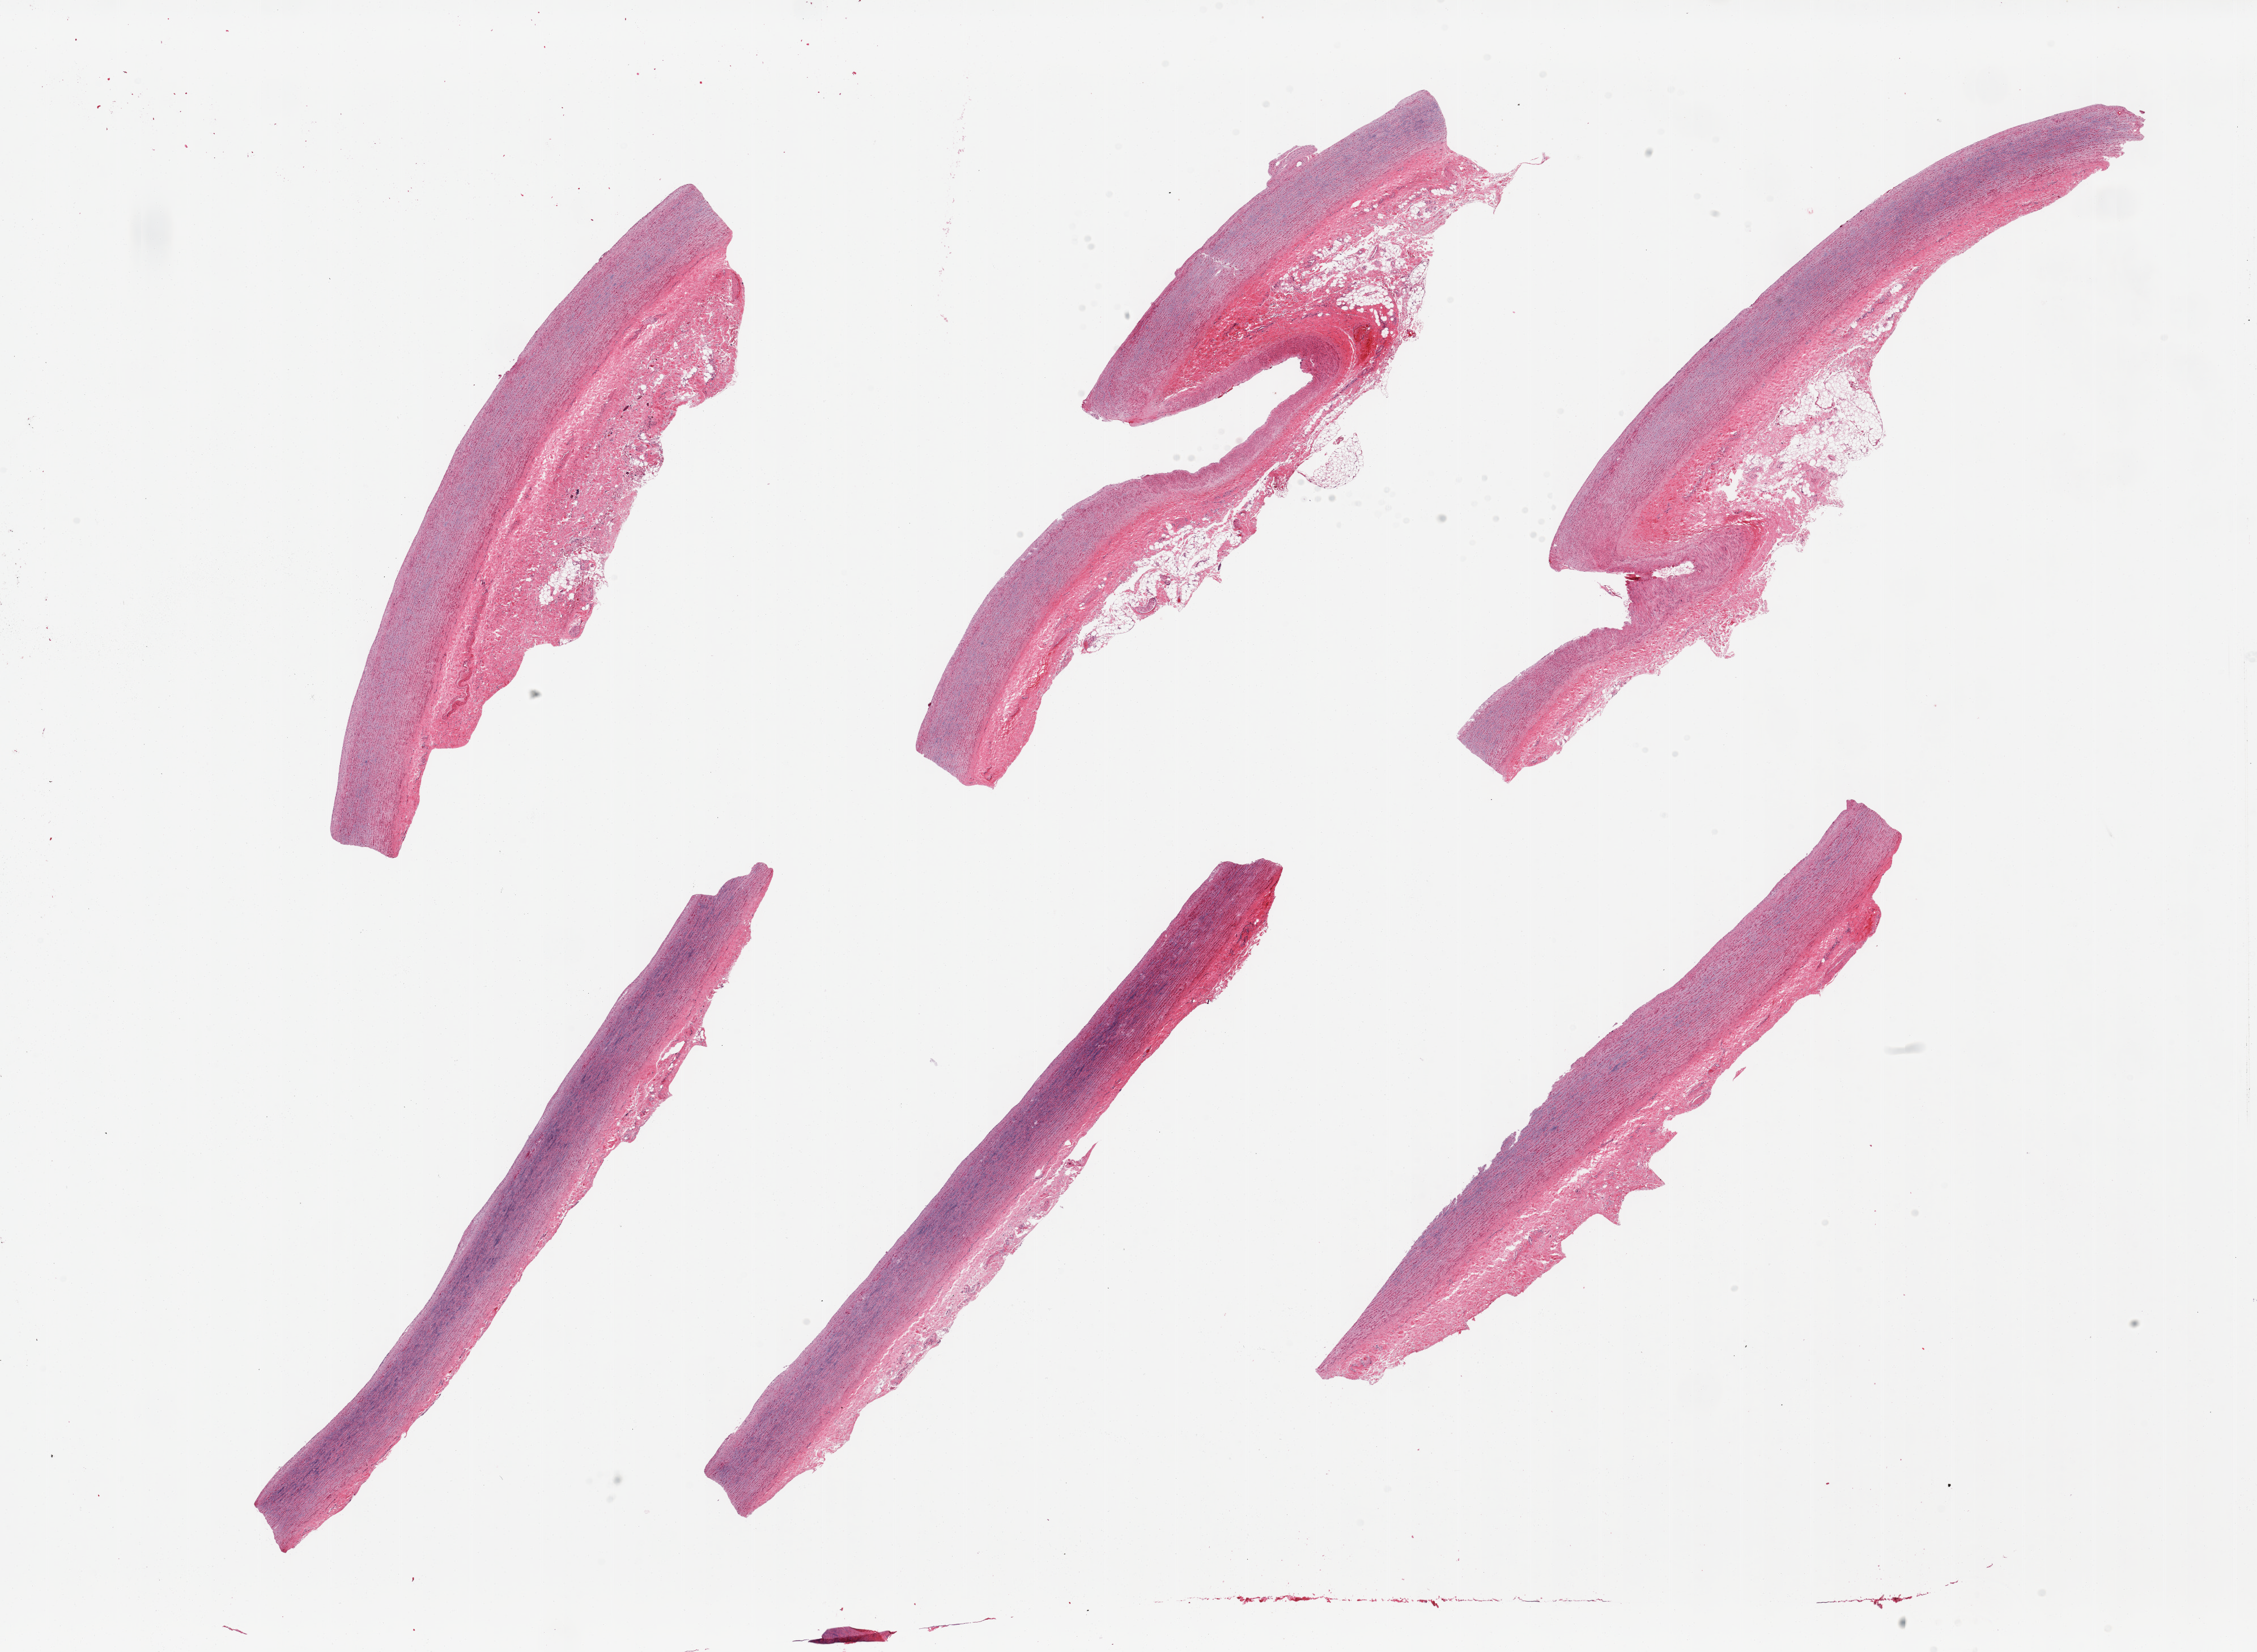
Digitized hematoxylin and eosin (H&E)-stained section — a low-resolution overview of the entire scanned area, about 31.5 x 23.1 mm. PAXgene-fixed, paraffin-embedded tissue. Section of aorta (target tissue). Tissue donor sample. Male donor.
Pathologist's review note for this sample: 6 pieces, adherent serosa/fat up to ~1.5mm; minimal atherosis.